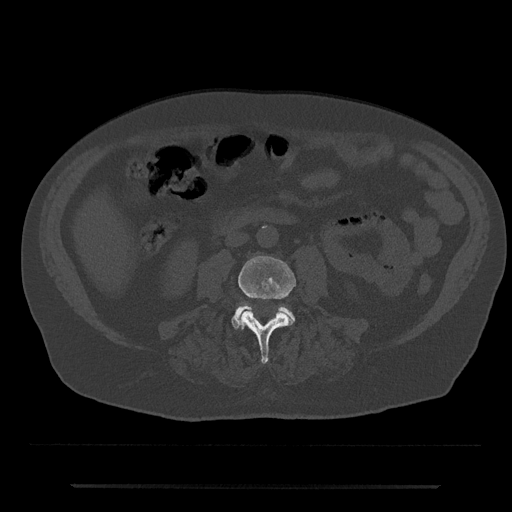
CT including the spine, one axial slice; position 392 of 797 along the scan axis; reconstruction kernel Br40s/3; 120 kVp; bone window (W 1800 / L 400 HU); 0.5 mm slice thickness; 512 × 512 image matrix, field of view 434 × 434 mm. Patient: male, 80 years. From the clinical record (not read from this slice): primary cancer: prostate; vertebrae with lytic lesions (as recorded): L1, T11.
Annotated regions visible in this slice (semi-automatic segmentation, software-assisted and operator-edited):
- L3 vertebra: box from (x=238, y=256) to (x=296, y=364) px
- L4 vertebra: (x=231, y=305)–(x=295, y=329)